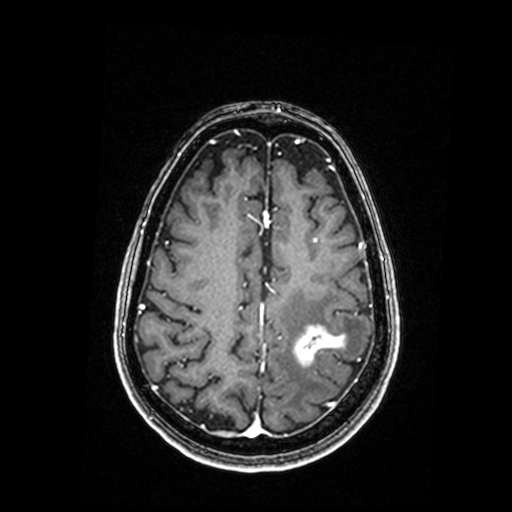
Brain MRI from a brain-tumour surgery series, one axial slice; slice 60 of 192 in the series (ordered by position); T1-weighted post-contrast; 0.98 mm slice thickness; 512 × 512 image matrix. Case-level facts recorded for this patient, not image findings: histopathology: Metastastic Carcinoma, Poorly Differentiated; tumour location: Left Parietal.
Annotated regions visible in this slice (manually delineated by an expert):
- tumour: bounding box <294,328,345,367> (left, top, right, bottom; pixels)